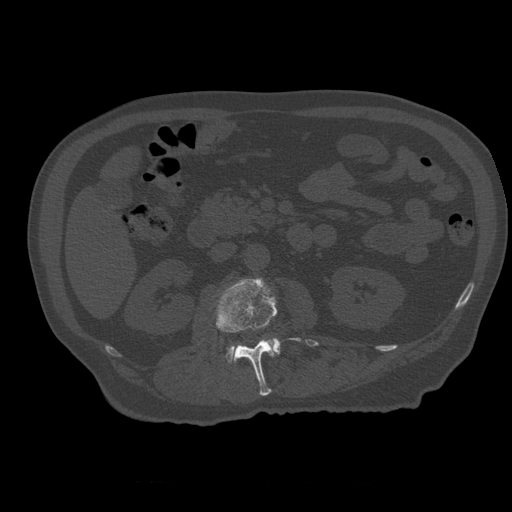
CT including the spine, one axial slice. Reconstruction kernel STANDARD. Bone window (W 1800 / L 400 HU). 512 × 512 image matrix. Patient age 73 years. Case-level facts recorded for this patient, not image findings: primary cancer: prostate; vertebrae with lytic lesions (as recorded): L2.
Annotated regions visible in this slice (semi-automatic segmentation, software-assisted and operator-edited):
- L2 vertebra: bounding box <216,278,302,396> (left, top, right, bottom; pixels)
- L3 vertebra: <226,337,281,363>